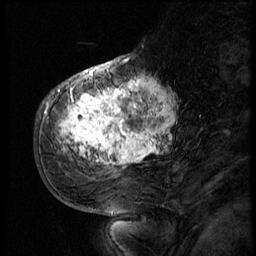
Breast MRI (dynamic contrast-enhanced), one sagittal slice. Position 21 of 56 along the scan axis. 3 images stored at this slice position (order not interpretable as contrast timing). 1.5 T. TE 4.2 ms, TR 9 ms. 2.5 mm slice thickness. 256 × 256 image matrix, field of view 180 × 180 mm. Female patient, age 51 years. From the clinical record (not read from this slice): setting: breast cancer imaged before/during neoadjuvant chemotherapy; receptor status: triple-negative.
Annotated regions visible in this slice (semi-automatic segmentation, software-assisted and operator-edited):
- analysis volume of interest (the breast-tissue region the enhancement analysis was run in; not a lesion): box from (x=52, y=66) to (x=183, y=179) px
- tumour enhancement mask (voxels above the 140 % enhancement threshold inside the analysis volume of interest): (x=57, y=72)–(x=176, y=167)